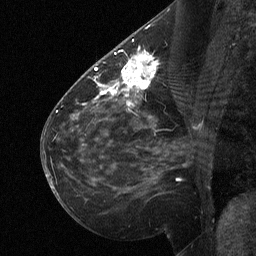
Breast MRI (dynamic contrast-enhanced), one sagittal slice; position 32 of 64 along the scan axis; dynamic contrast-enhanced study with each time point stored as its own series, time point 2 of 3 at this slice position (early post-contrast, ordered by acquisition time); 1.5 T; TE 4.8 ms, TR 27 ms; 256 × 256 image matrix, field of view 200 × 200 mm. Patient: female, 51 years. From the clinical record (not read from this slice): setting: breast cancer imaged before/during neoadjuvant chemotherapy; receptor status: HR-positive, HER2-negative.
Annotated regions visible in this slice (semi-automatic segmentation, software-assisted and operator-edited):
- analysis volume of interest (the breast-tissue region the enhancement analysis was run in; not a lesion): box from (x=112, y=46) to (x=158, y=106) px
- tumour enhancement mask (voxels above the 90 % enhancement threshold inside the analysis volume of interest): (x=112, y=52)–(x=157, y=104)